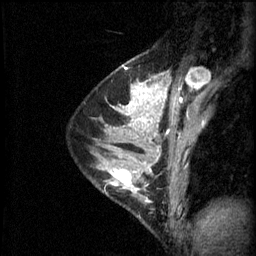
Breast MRI (dynamic contrast-enhanced), one sagittal slice. Position 38 of 60 along the scan axis. 3 images stored at this slice position (order not interpretable as contrast timing). 1.5 T. TE 4.2 ms, TR 11 ms. 256 × 256 image matrix, field of view 180 × 180 mm. Female patient, age 29 years.
Outlined on this slice (semi-automatic segmentation, software-assisted and operator-edited):
- analysis volume of interest (the breast-tissue region the enhancement analysis was run in; not a lesion): bounding box <97,164,153,223> (left, top, right, bottom; pixels)
- tumour enhancement mask (voxels above the 70 % enhancement threshold inside the analysis volume of interest): <107,168,150,203>